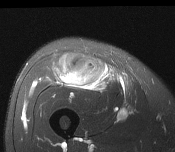
MRI of an extremity soft-tissue mass, one axial slice. Slice 70 of 116 in the series (ordered by position). T2-weighted fat-saturated. MR volume resampled by the dataset authors to the PET/CT grid (not the native acquisition matrix). 3.27 mm slice thickness. 175 × 152 image matrix, field of view 171 × 148 mm. Male patient. From the clinical record (not read from this slice): histological type: pleiomorphic leiomyosarcoma; grade: intermediate; site of the primary tumour: right thigh.
Outlined on this slice (expert contour drawn on MRI and transferred to this co-registered scan by the dataset authors):
- gross tumour volume including surrounding oedema: bounding box <54,54,109,89> (left, top, right, bottom; pixels)
- gross tumour volume (mass): <67,61,103,87>